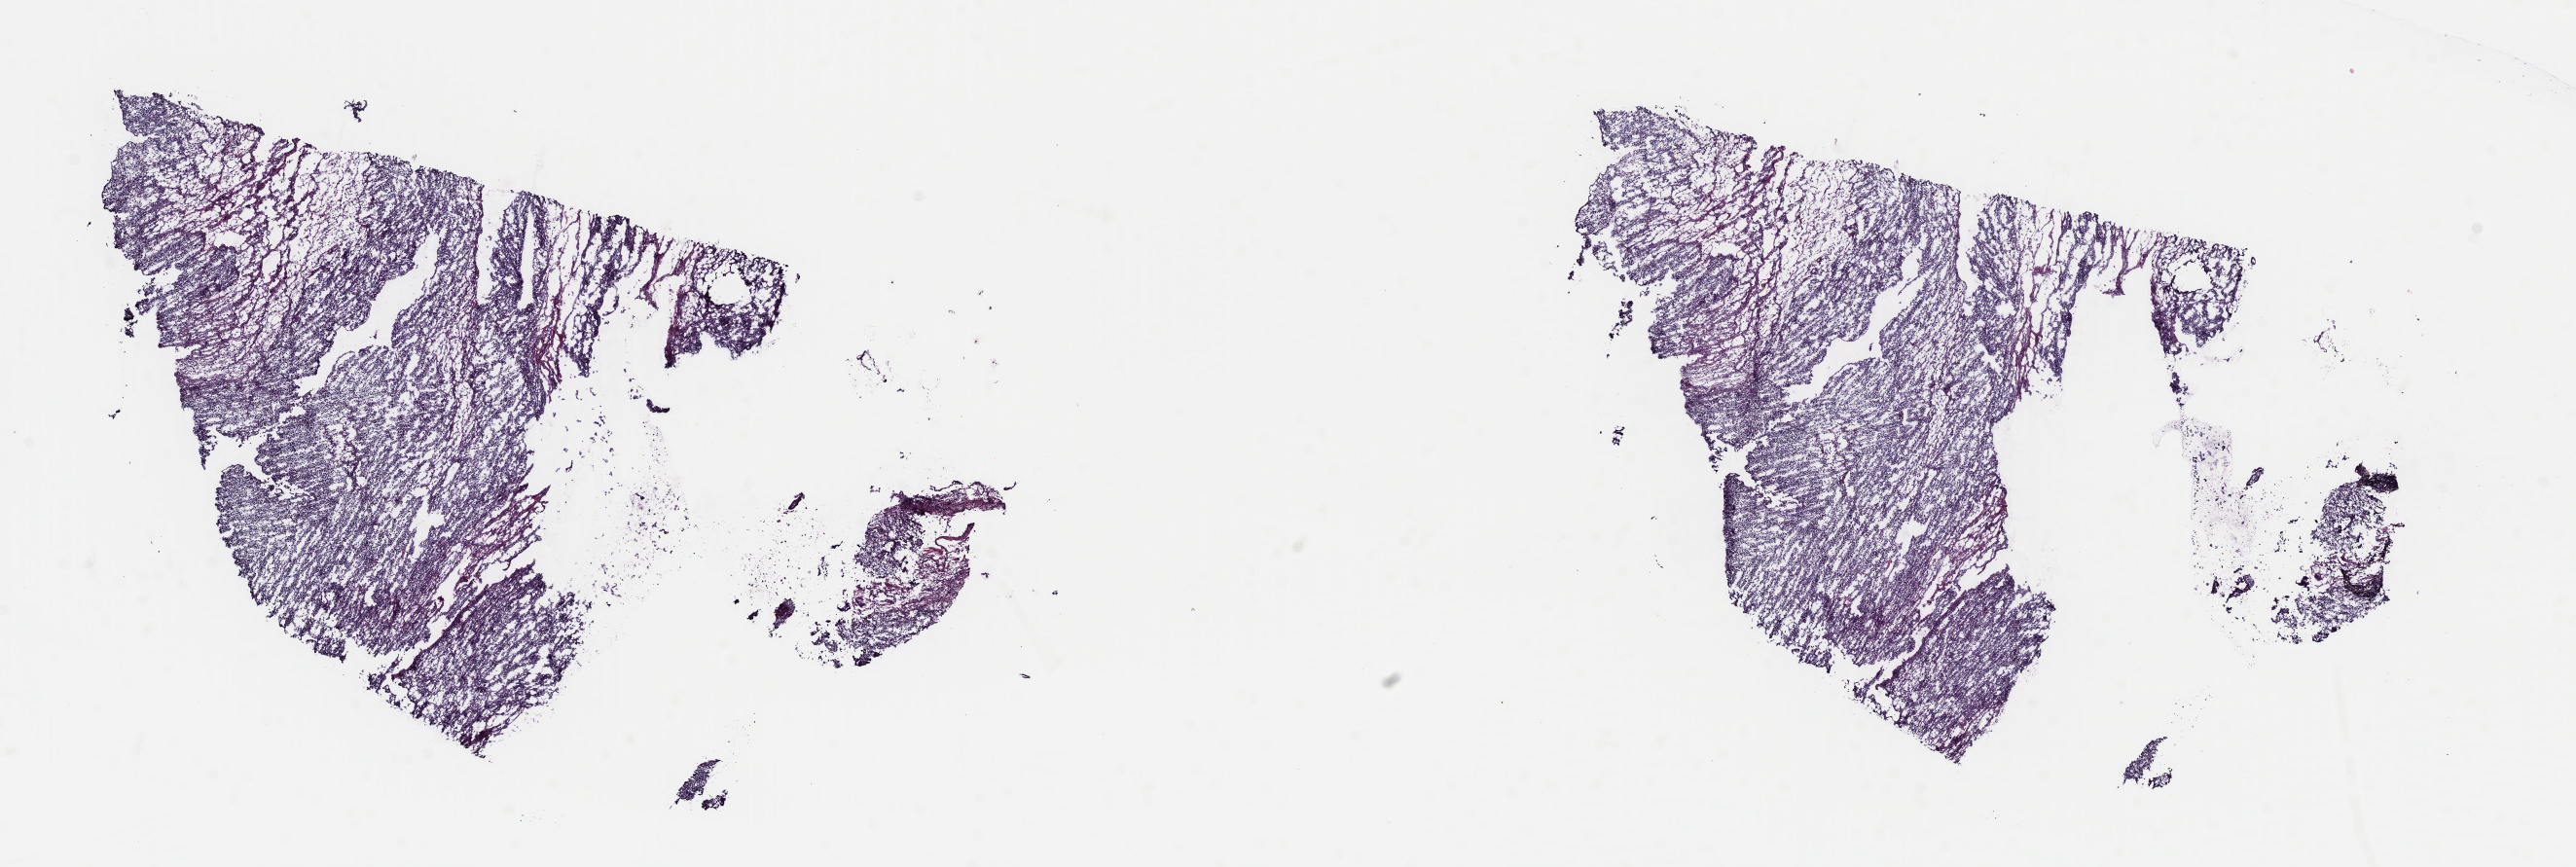
Whole-slide histology image, H&E-stained, whole scanned area (about 20.9 x 7.0 mm, acquisition: 40x scan) shown as a low-resolution overview, frozen section from the top of the tissue portion, uterus, primary tumour sample. Female, age 71 years at initial diagnosis. Pathologist review of this section (percent, as recorded): tumour cells 80%, tumour nuclei 90%, normal cells 0%, stromal cells 10%, necrosis 10%. Infiltration values recorded for this section: lymphocyte infiltration 0%, monocyte infiltration 0%, neutrophil infiltration 0%.
• FIGO stage: IVB
• diagnosis: Mullerian mixed tumor (endometrium)